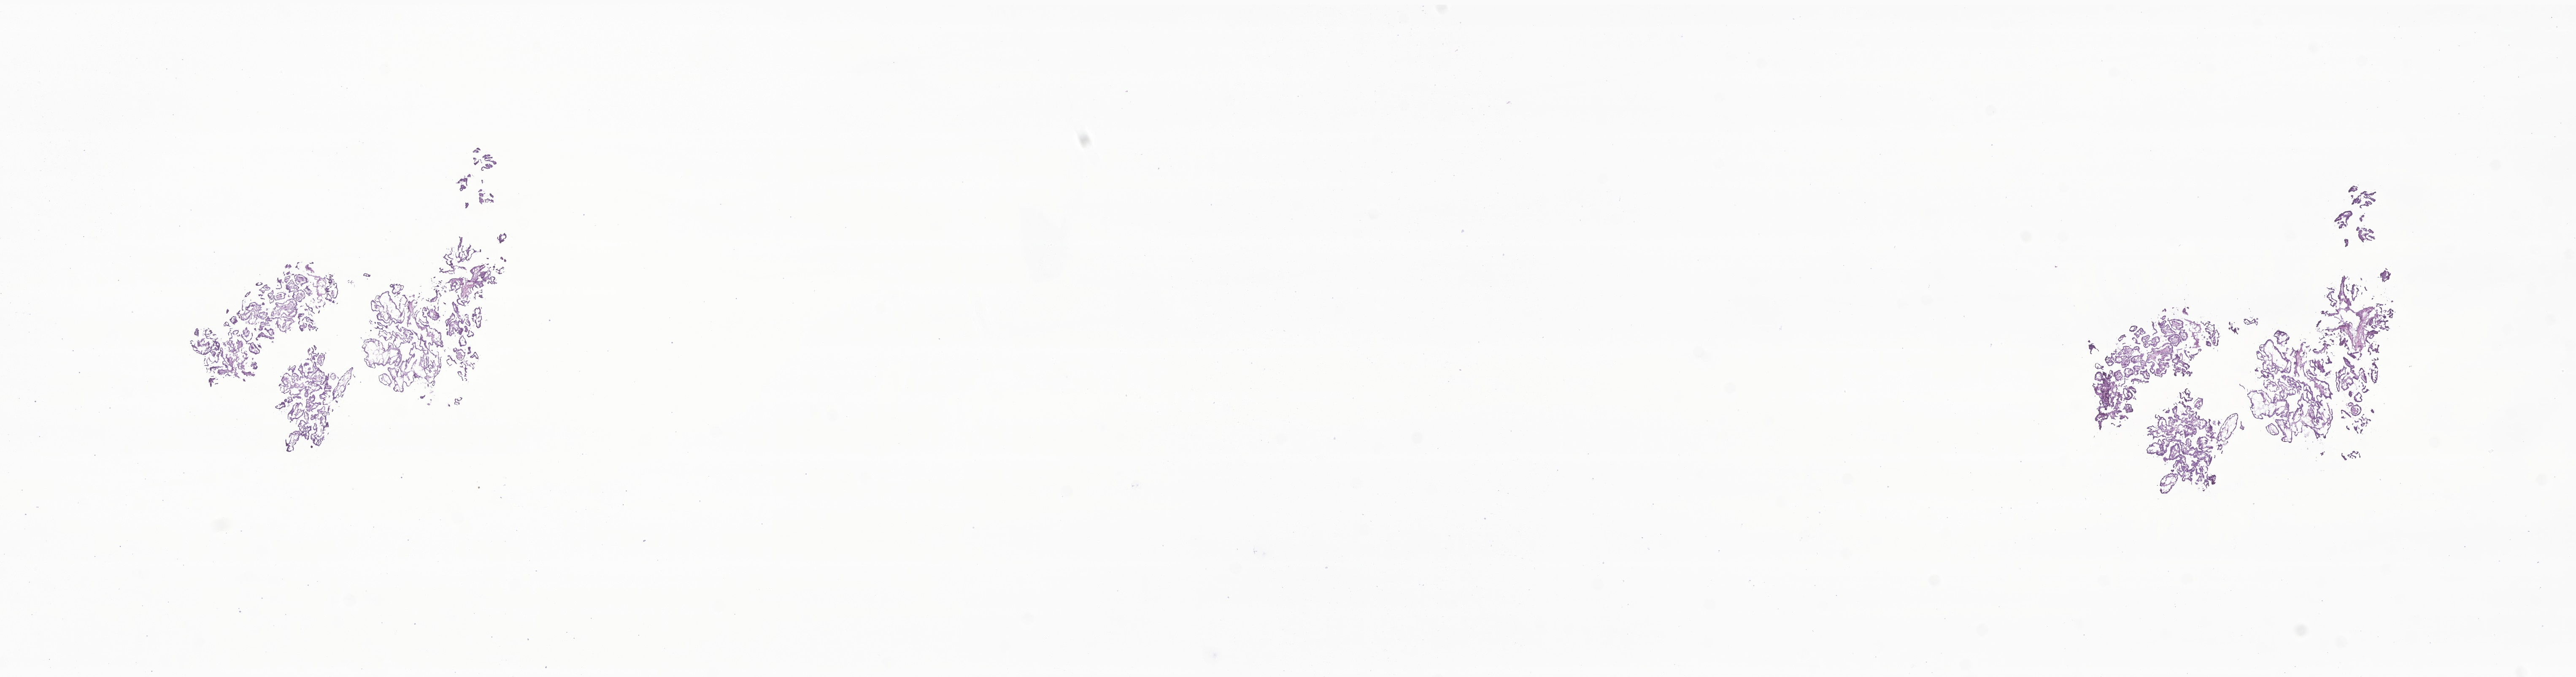
H&E whole-slide image of tumor tissue from the thyroid, whole scanned area (about 25.7 x 6.8 mm) shown as a low-resolution overview, cryosection (OCT / tissue freezing medium). Patient female; age 199 months (16 years 7 months).
Diagnosis (ICD-O-3 morphology term): Papillary carcinoma, NOS.